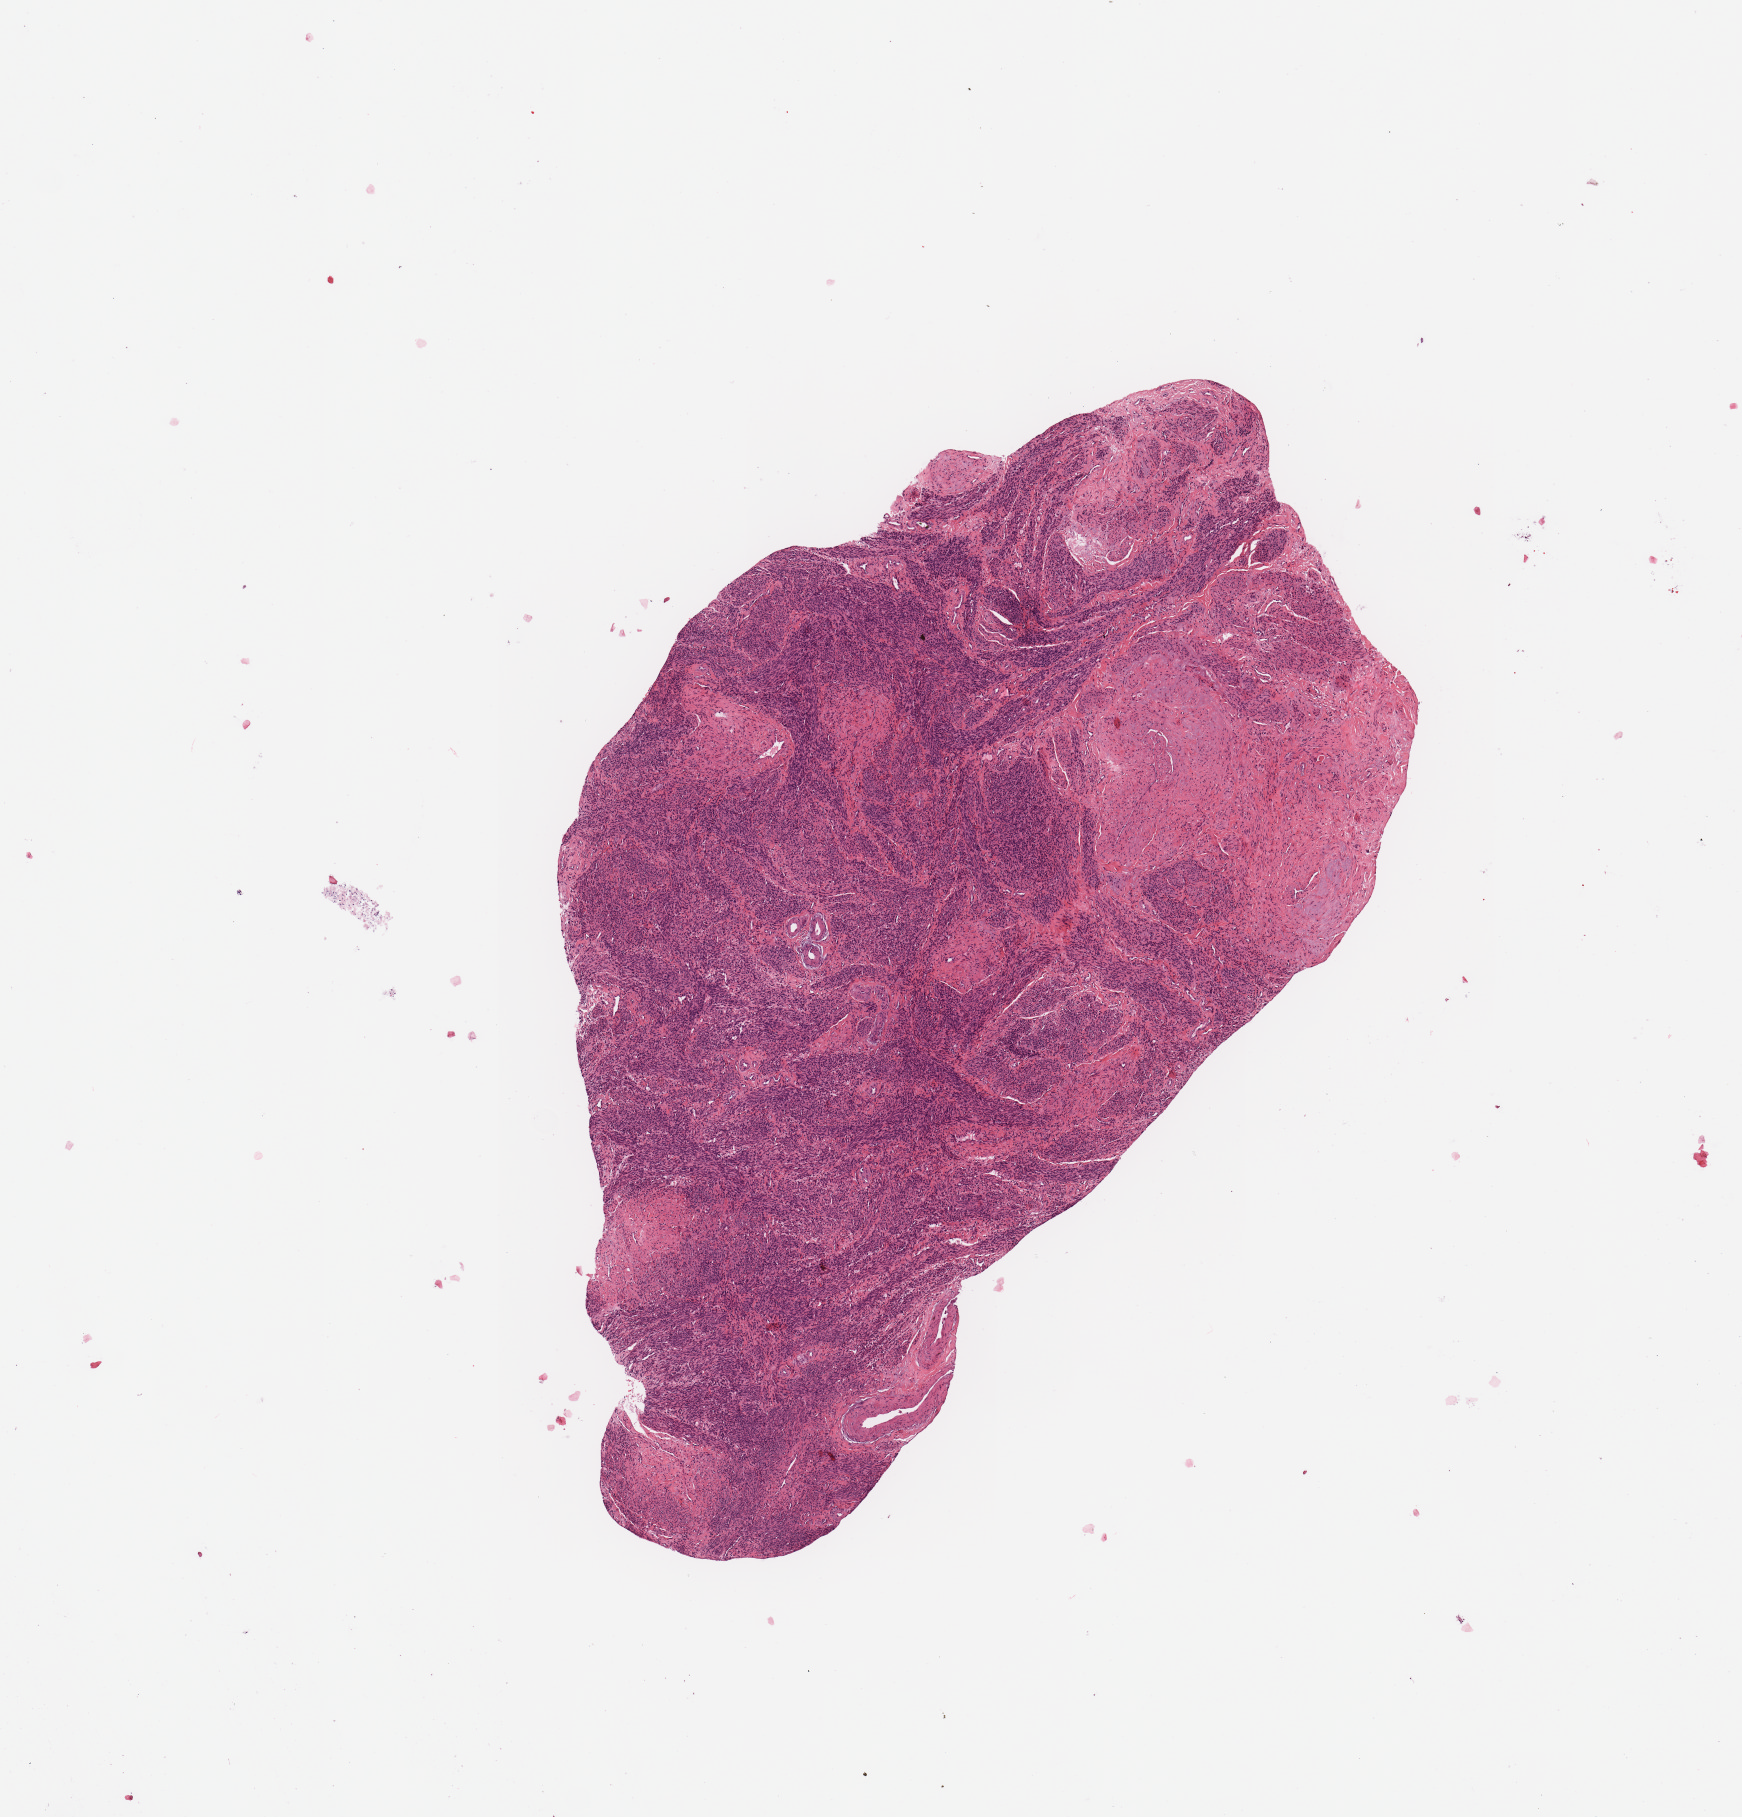
Hematoxylin and eosin (H&E) stained whole-slide image, a low-resolution overview of the entire scanned area, about 6.9 x 7.2 mm (from a 20x scan). Normal (non-tumour) tissue sample, sampled site: uterus. 73-year-old female patient.
- this section: normal (non-tumour) tissue from the same patient
- patient diagnosis: Endometrioid adenocarcinoma, NOS